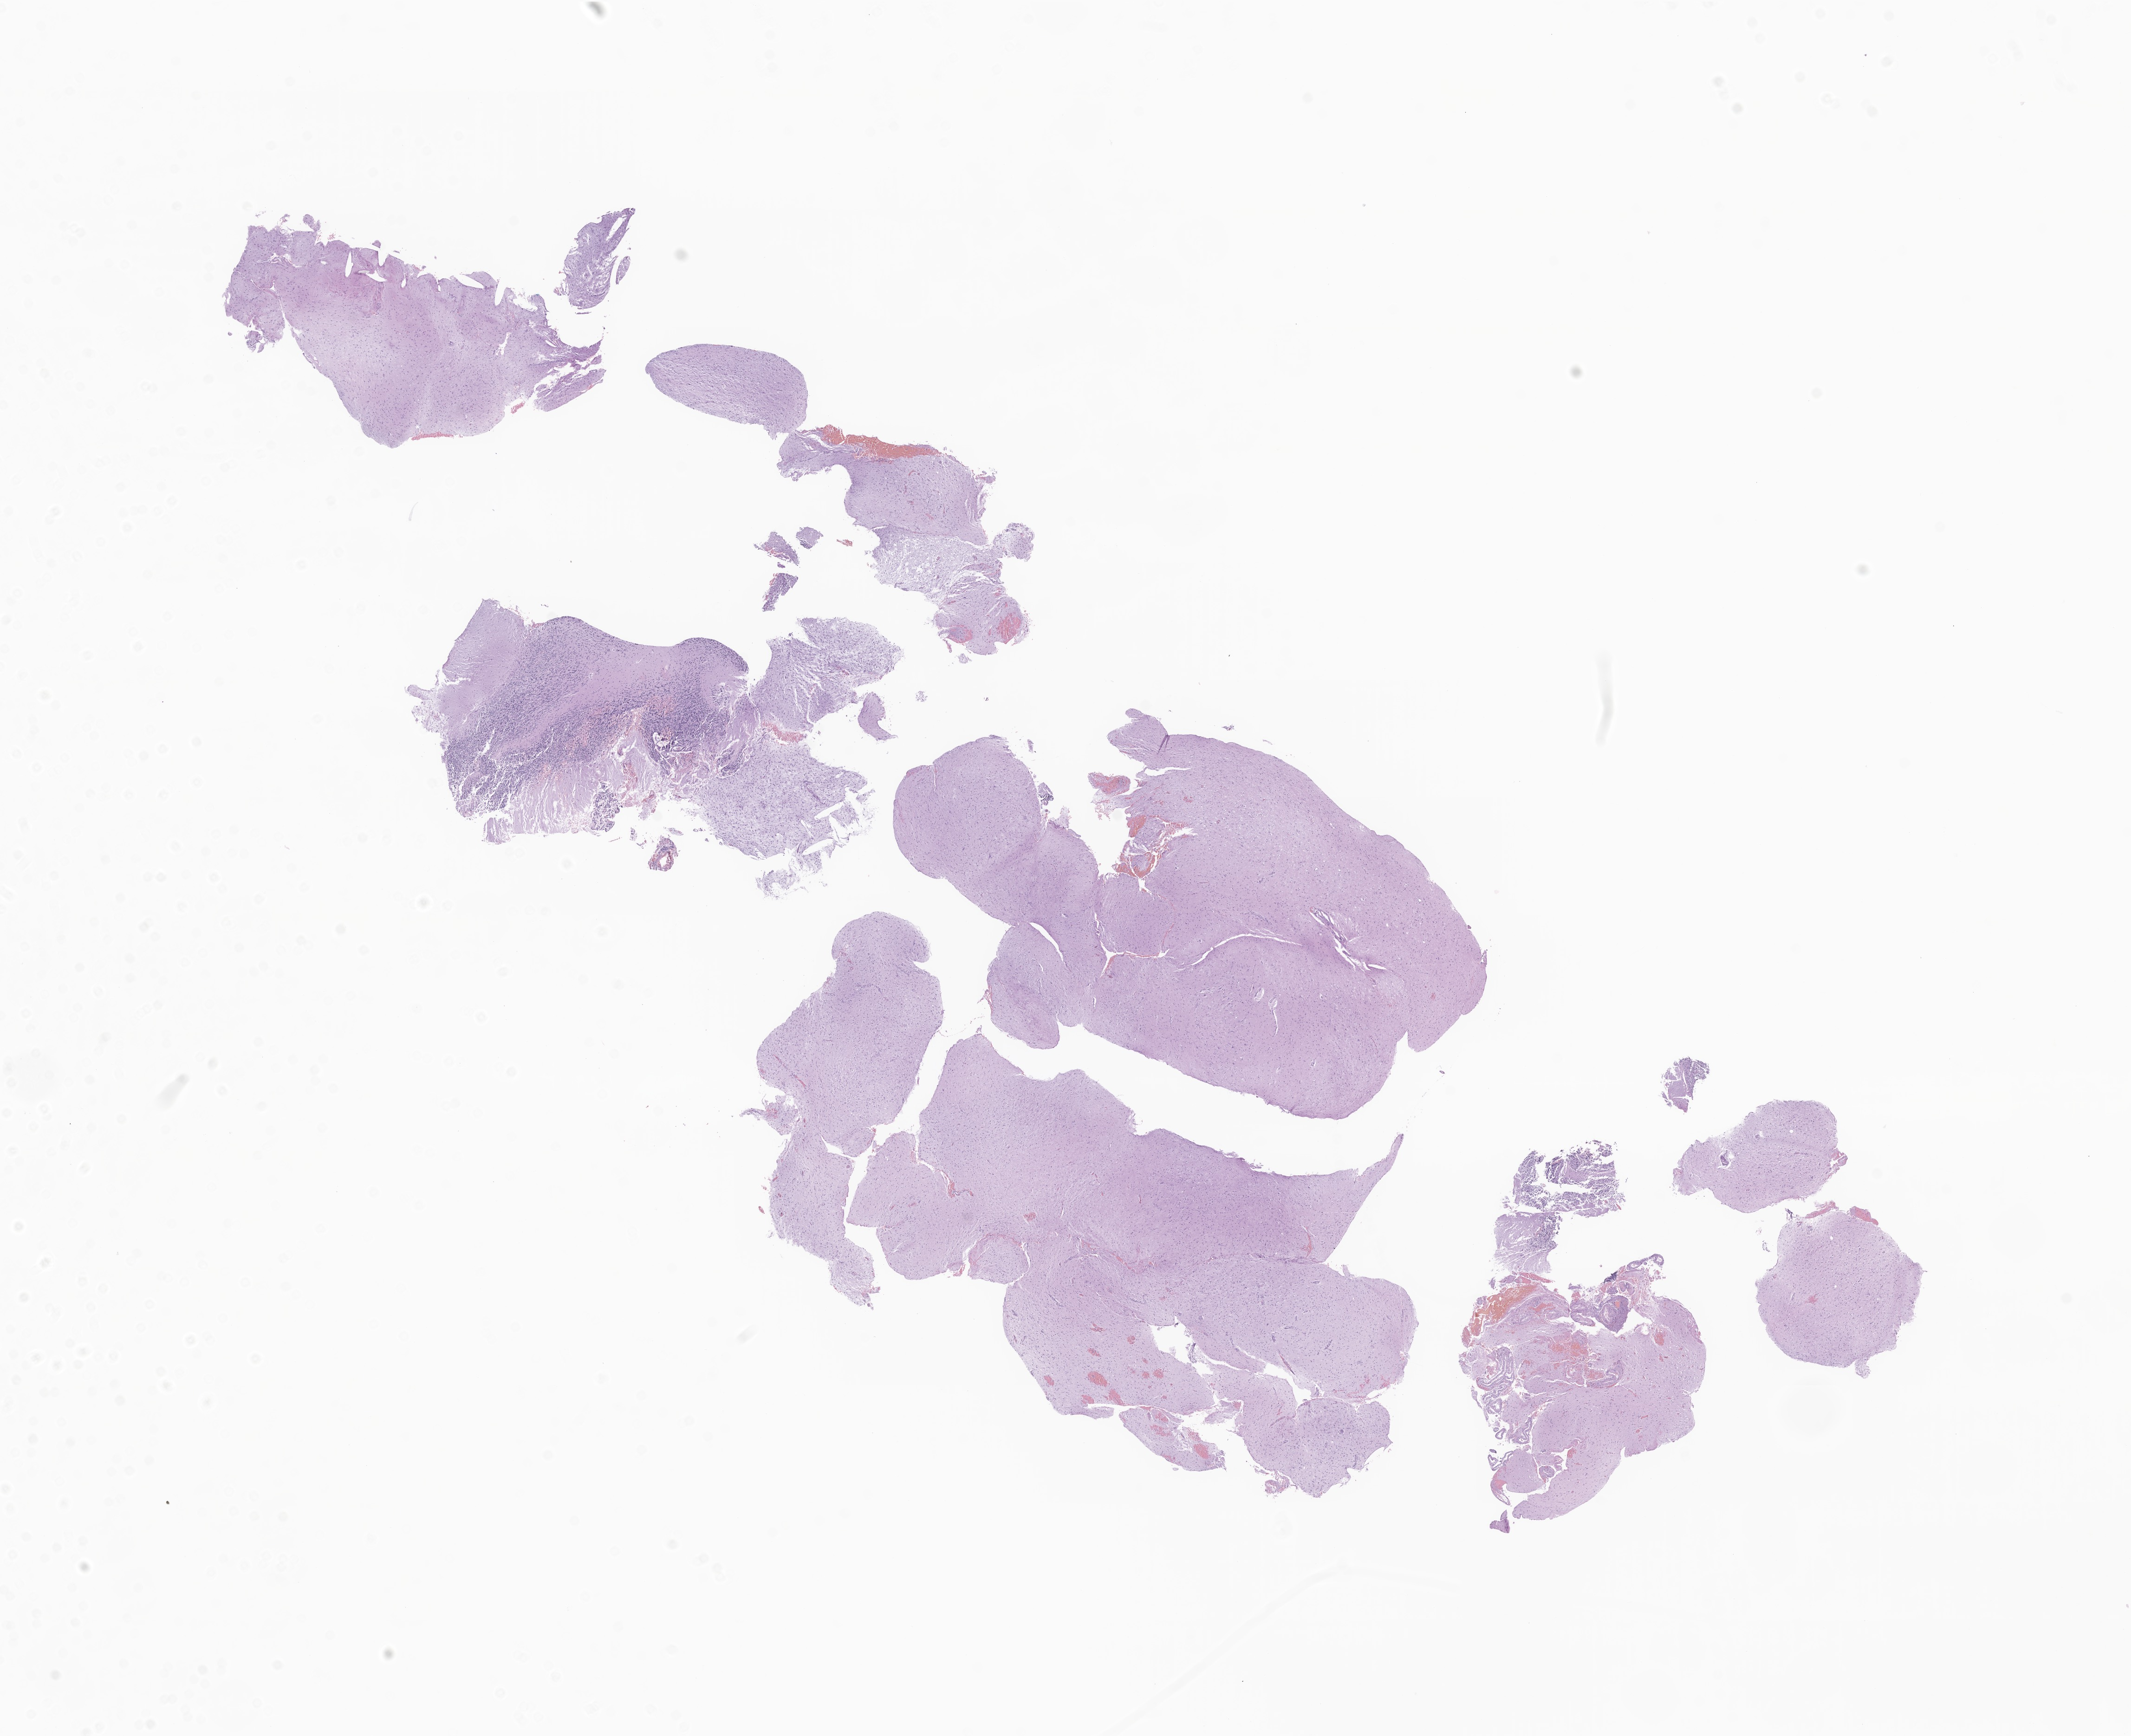
Digitized haematoxylin and eosin-stained section of tumor tissue from the cerebellum — low-resolution overview of the scanned area, about 19.3 x 15.8 mm, formalin-fixed paraffin-embedded section. Patient male; age 777 days (about 2.1 years).
Diagnosis (ICD-O-3 morphology term): Pilocytic astrocytoma.